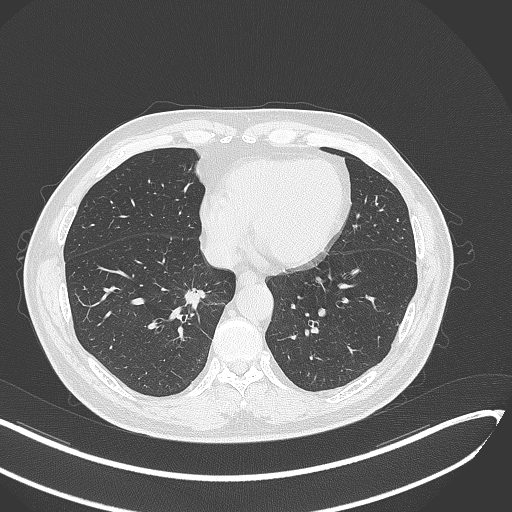
Chest CT, one axial slice. Slice 128 of 429 in the series (ordered by position). 120 kVp. Lung window (W 1500 / L -600 HU). 1 mm slice thickness. 512 × 512 image matrix. Male patient, age 62 years. From the clinical record (not read from this slice): clinical TNM (as recorded): T1b N0 M0.
Outlined on this slice (bounding box drawn by a radiologist):
- lung tumour (recorded histology: adenocarcinoma): bounding box [x1, y1, x2, y2] px = [183, 285, 222, 319]